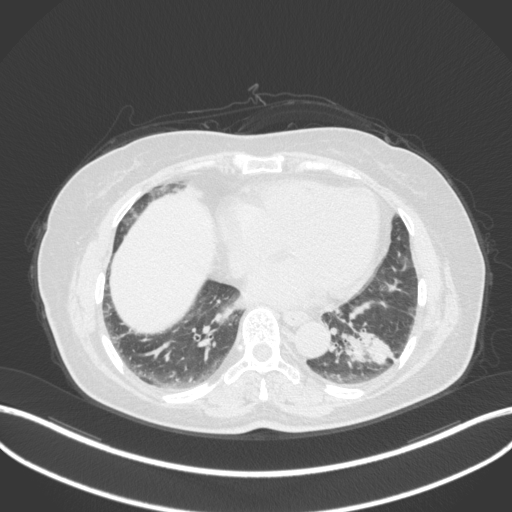
Chest CT, one axial slice. Reconstruction kernel B31f. Lung window (W 1500 / L -600 HU). 512 × 512 image matrix. Female patient, age 59 years. Case-level facts recorded for this patient, not image findings: clinical TNM (as recorded): T2a N0 M0; histopathological grade: G2-3.
Structures marked on this image (rectangle marked by the reading radiologist):
- lung tumour (recorded histology: adenocarcinoma): bounding box [x1, y1, x2, y2] px = [338, 321, 398, 372]